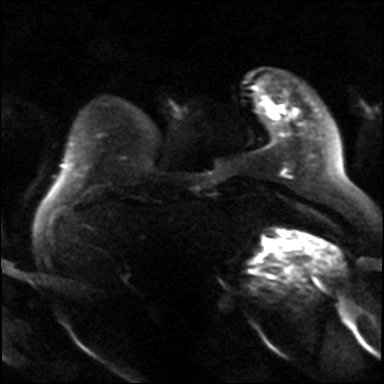
Breast MRI, one axial slice. Slice 5 of 36 in the series (ordered by position). Diffusion-weighted series; image 2 of 4 stored at this slice position (different b-values; order by instance number). 3 T. 4 mm slice thickness. 384 × 384 image matrix, field of view 320 × 320 mm. Female patient.
Structures marked on this image (outlined manually by an expert reader):
- tumour on diffusion-weighted imaging: bounding box <270,105,284,114> (left, top, right, bottom; pixels)